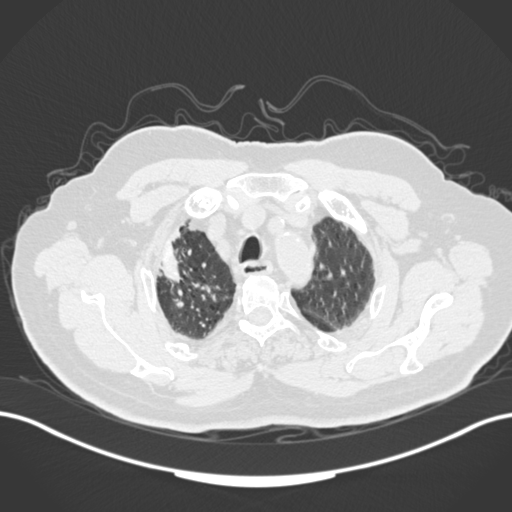
Chest CT, one axial slice. Slice 141 of 205 in the series (ordered by position). Lung window (W 1500 / L -600 HU). 1 mm slice thickness. 512 × 512 image matrix, field of view 400 × 400 mm. Patient: male, 72 years. Case-level facts recorded for this patient, not image findings: clinical TNM (as recorded): T1a N0 M0.
Annotated regions visible in this slice (bounding box drawn by a radiologist):
- lung tumour (recorded histology: squamous cell carcinoma): bounding box <156,230,186,286> (left, top, right, bottom; pixels)